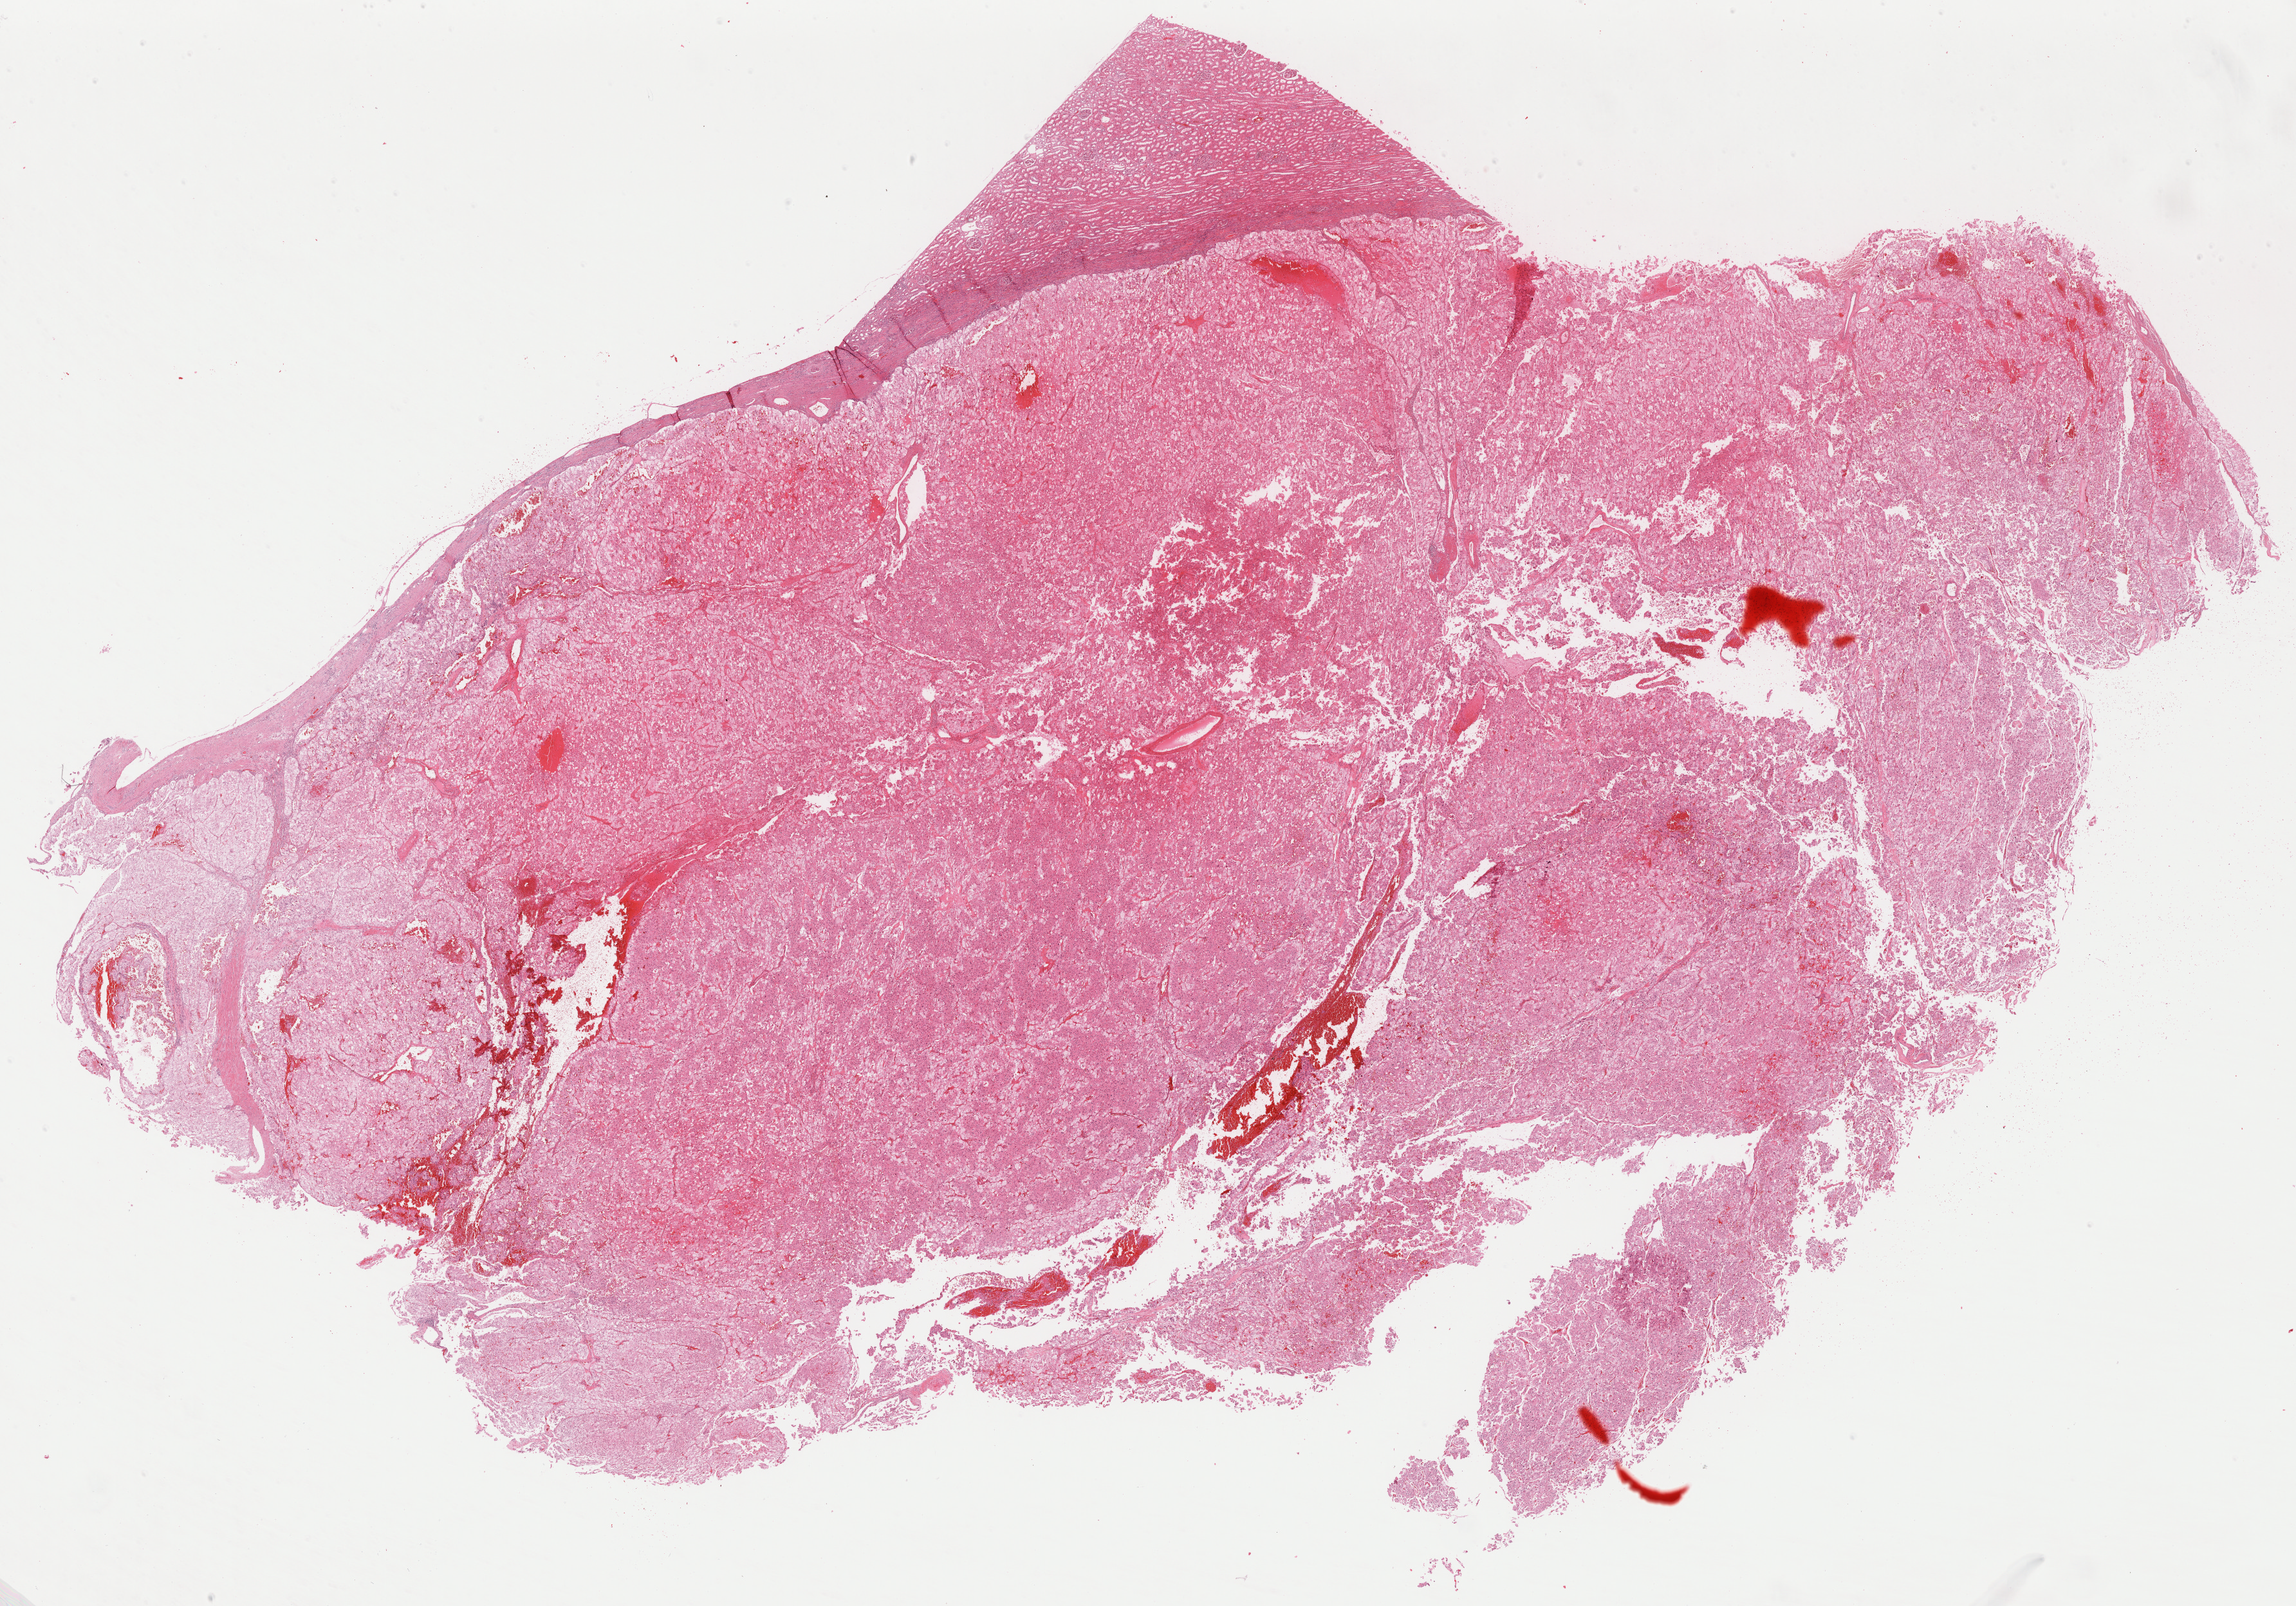
Whole-slide histology image, Hematoxylin and eosin (H&E) stained, low-resolution overview of the scanned area, about 28.8 x 20.1 mm (acquisition: 40x scan), formalin-fixed paraffin-embedded (FFPE) diagnostic section, kidney, primary tumour sample. Female, age 42 years at initial diagnosis.
AJCC pathologic stage: I. Pathologic diagnosis: Renal cell carcinoma, chromophobe type. Laterality: right.